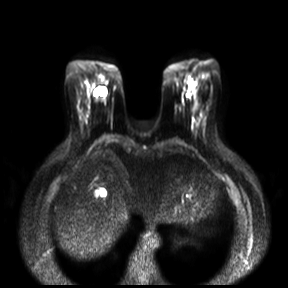
Breast MRI, one axial slice; slice 8 of 30 in the series (ordered by position); diffusion-weighted series; image 2 of 4 stored at this slice position (different b-values; order by instance number); 3 T; 288 × 288 image matrix. Female patient.
Annotated regions visible in this slice (outlined manually by an expert reader):
- tumour on diffusion-weighted imaging: bounding box (x1, y1, x2, y2) in pixels: (189, 84, 195, 91)